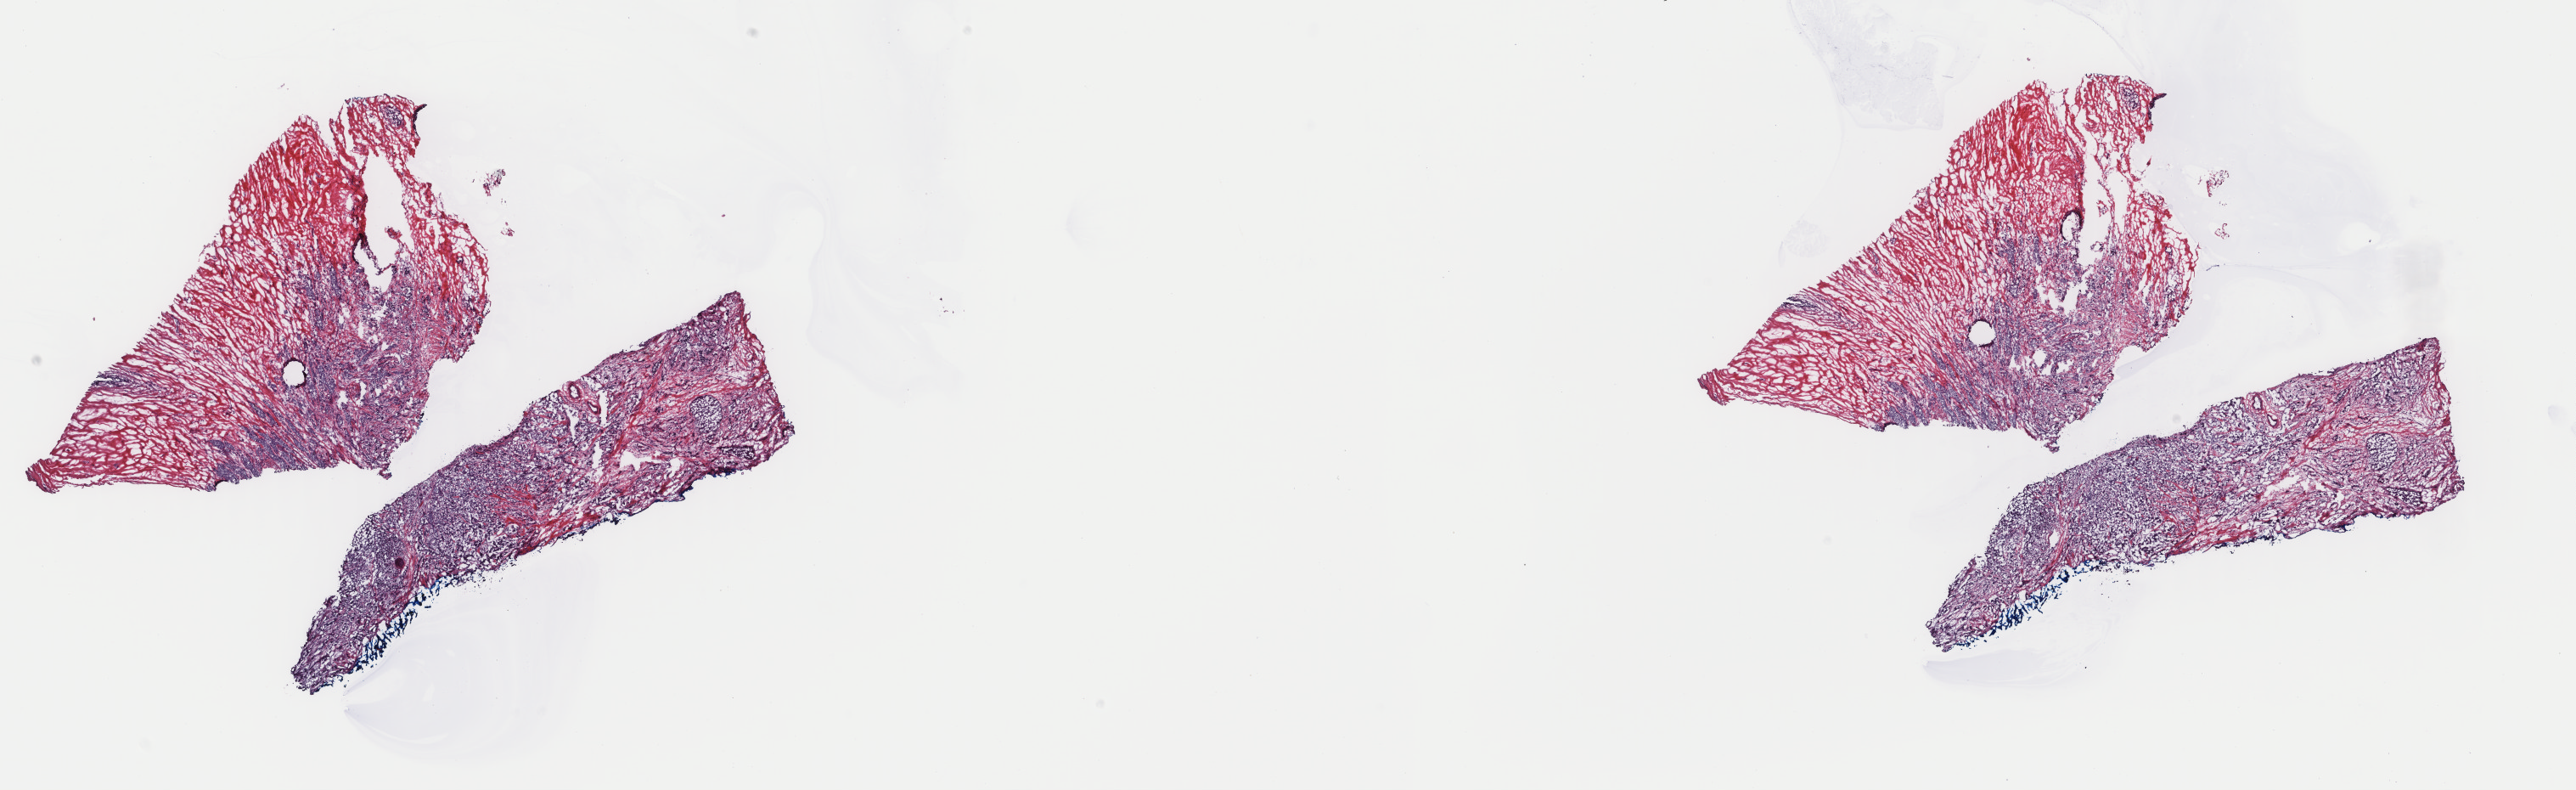
Whole-slide histology image, Hematoxylin and eosin (H&E) stained, a low-resolution overview of the entire scanned area, about 24.1 x 7.4 mm, frozen section from the top of the tissue portion, sample: primary tumour, breast. Patient: female, age at initial diagnosis 53 years. Composition of this section per pathologist review: tumour cells 70%, tumour nuclei 85%, normal cells 30%, stromal cells 0%, necrosis 0%. Infiltration values recorded for this section: lymphocyte infiltration 2%, monocyte infiltration 0%, neutrophil infiltration 0%.
AJCC pathologic stage: IA (7th edition). Histologic diagnosis: Lobular carcinoma, NOS.